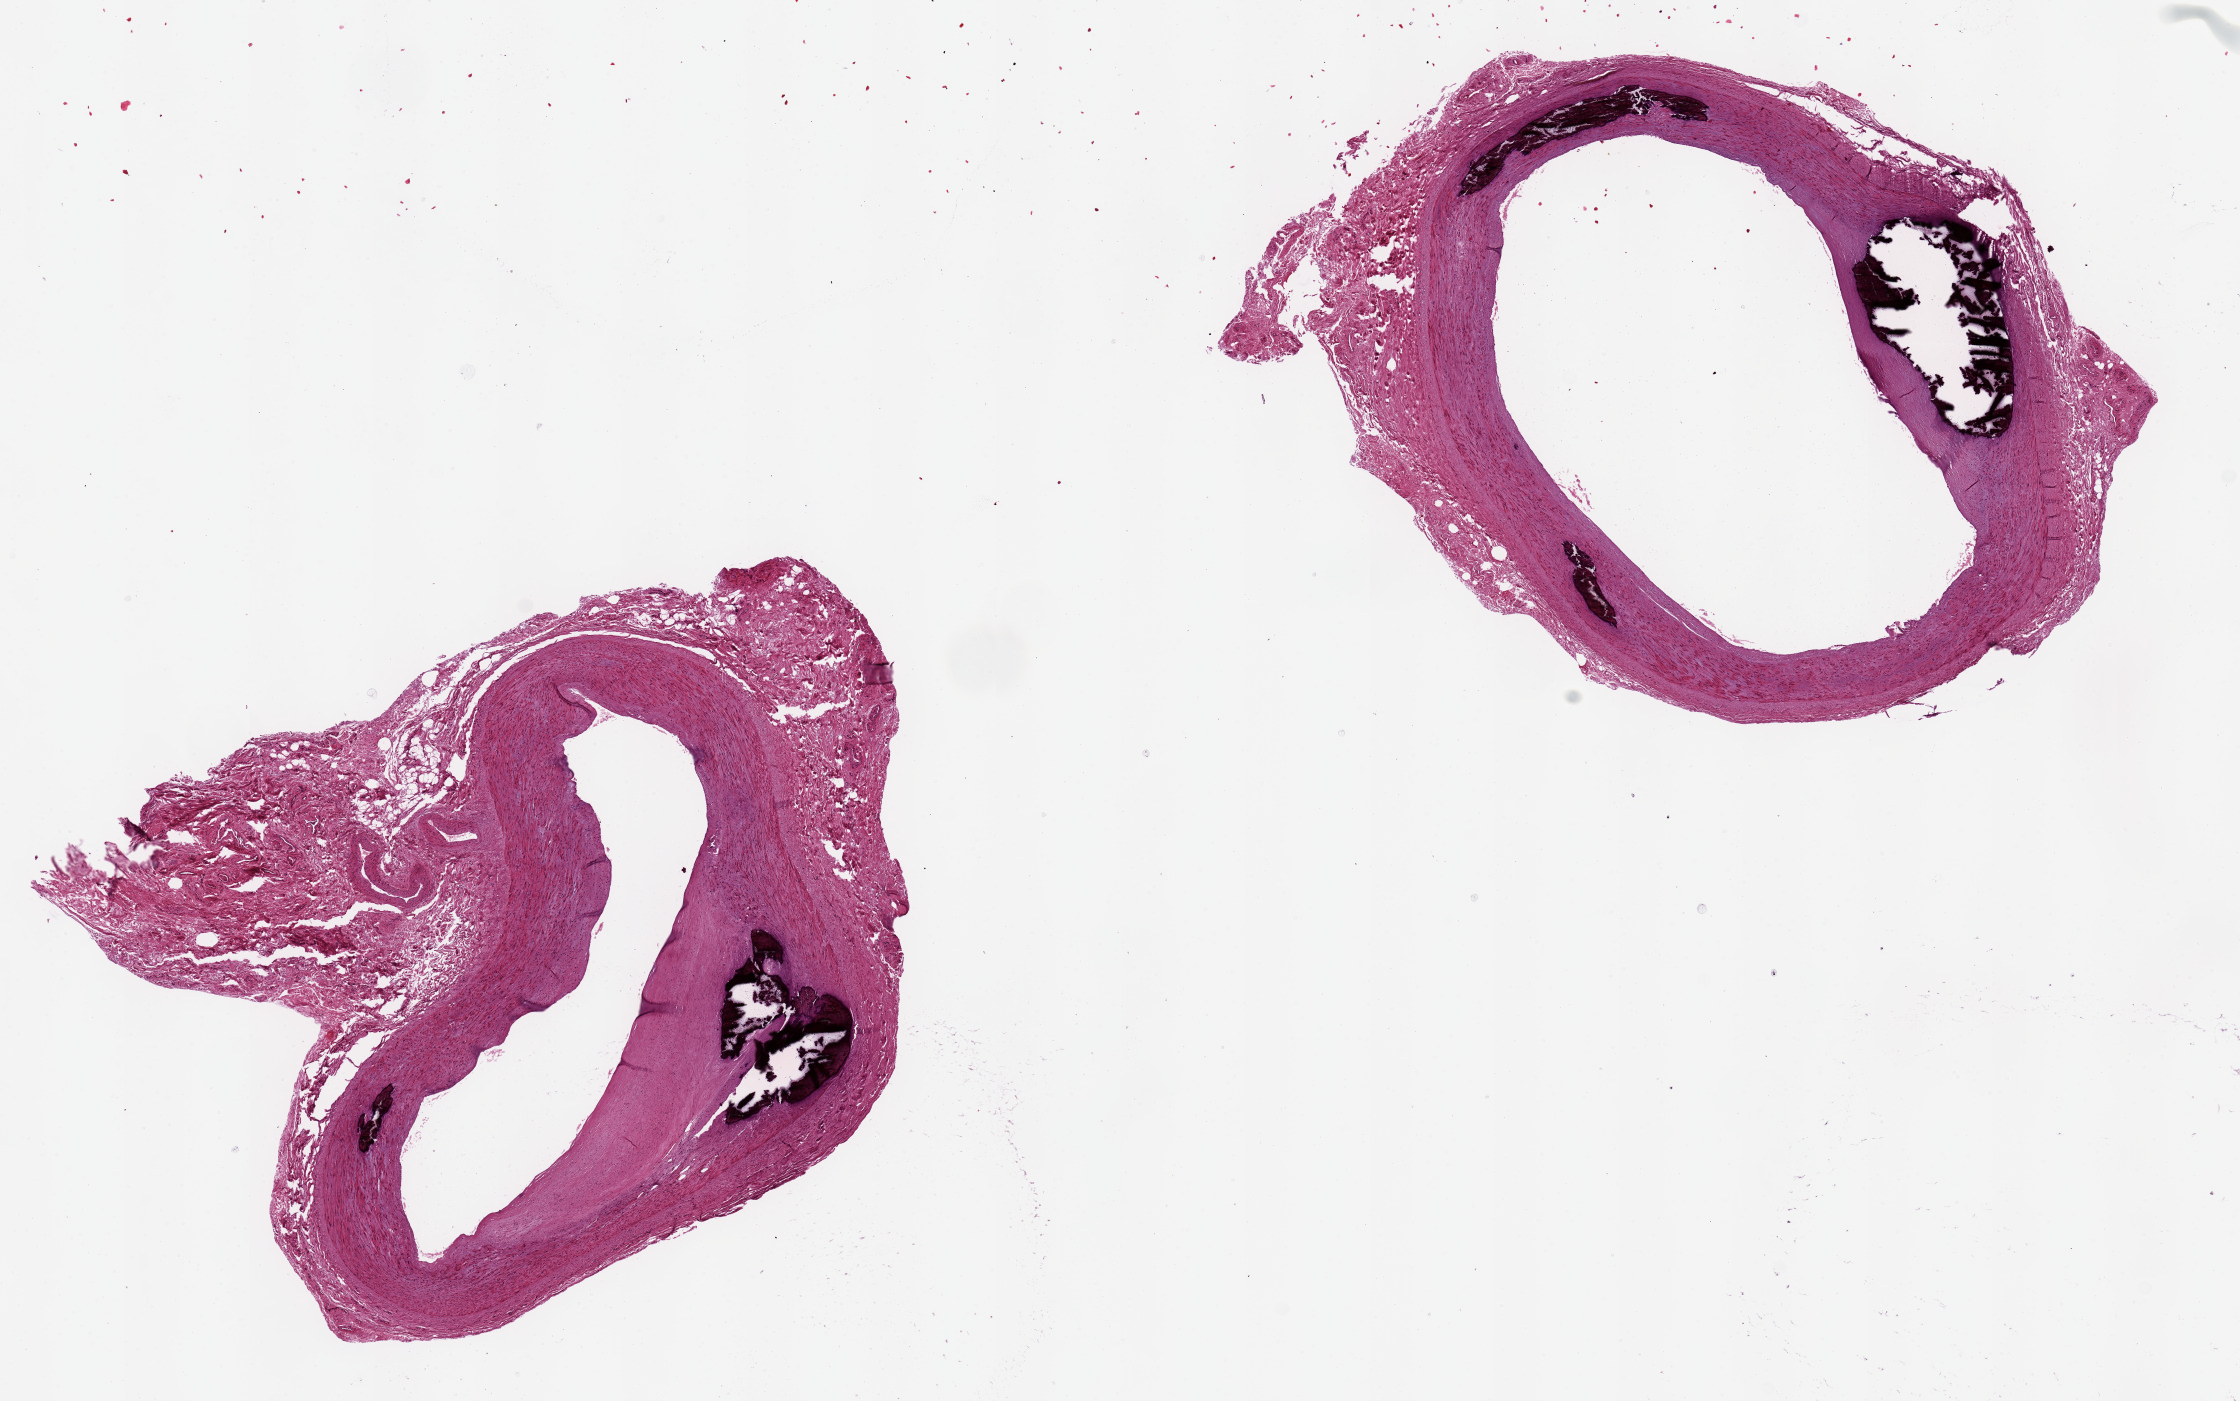
Whole-slide image, haematoxylin and eosin stain, brightfield — whole scanned area (about 17.7 x 11.1 mm) shown as a low-resolution overview; PAXgene-fixed, paraffin-embedded tissue; sampled site (target tissue): tibial artery; tissue donor sample.
Pathologist's review note for this sample: Clean specimen; Monckeberg???s medial sclerosis, multifocal.